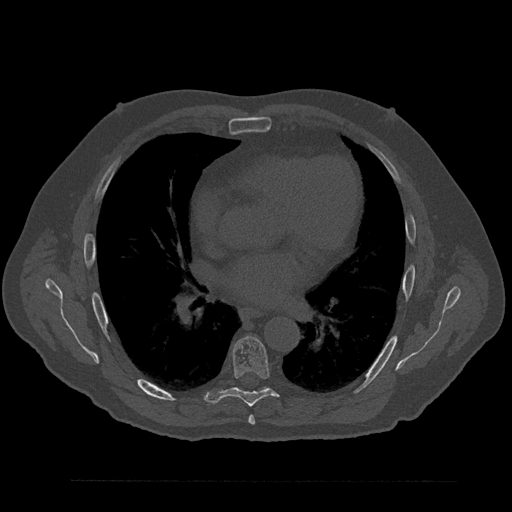
CT including the spine, one axial slice. Slice 505 of 797 in the series (ordered by position). 120 kVp. Bone window (W 1800 / L 400 HU). 0.5 mm slice thickness. 512 × 512 image matrix, field of view 430 × 430 mm. Male patient, age 61 years. From the clinical record (not read from this slice): primary cancer: prostate.
Outlined on this slice (semi-automatic segmentation, software-assisted and operator-edited):
- T6 vertebra: bounding box [x1, y1, x2, y2] px = [248, 416, 255, 425]
- T7 vertebra: [205, 336, 279, 407]